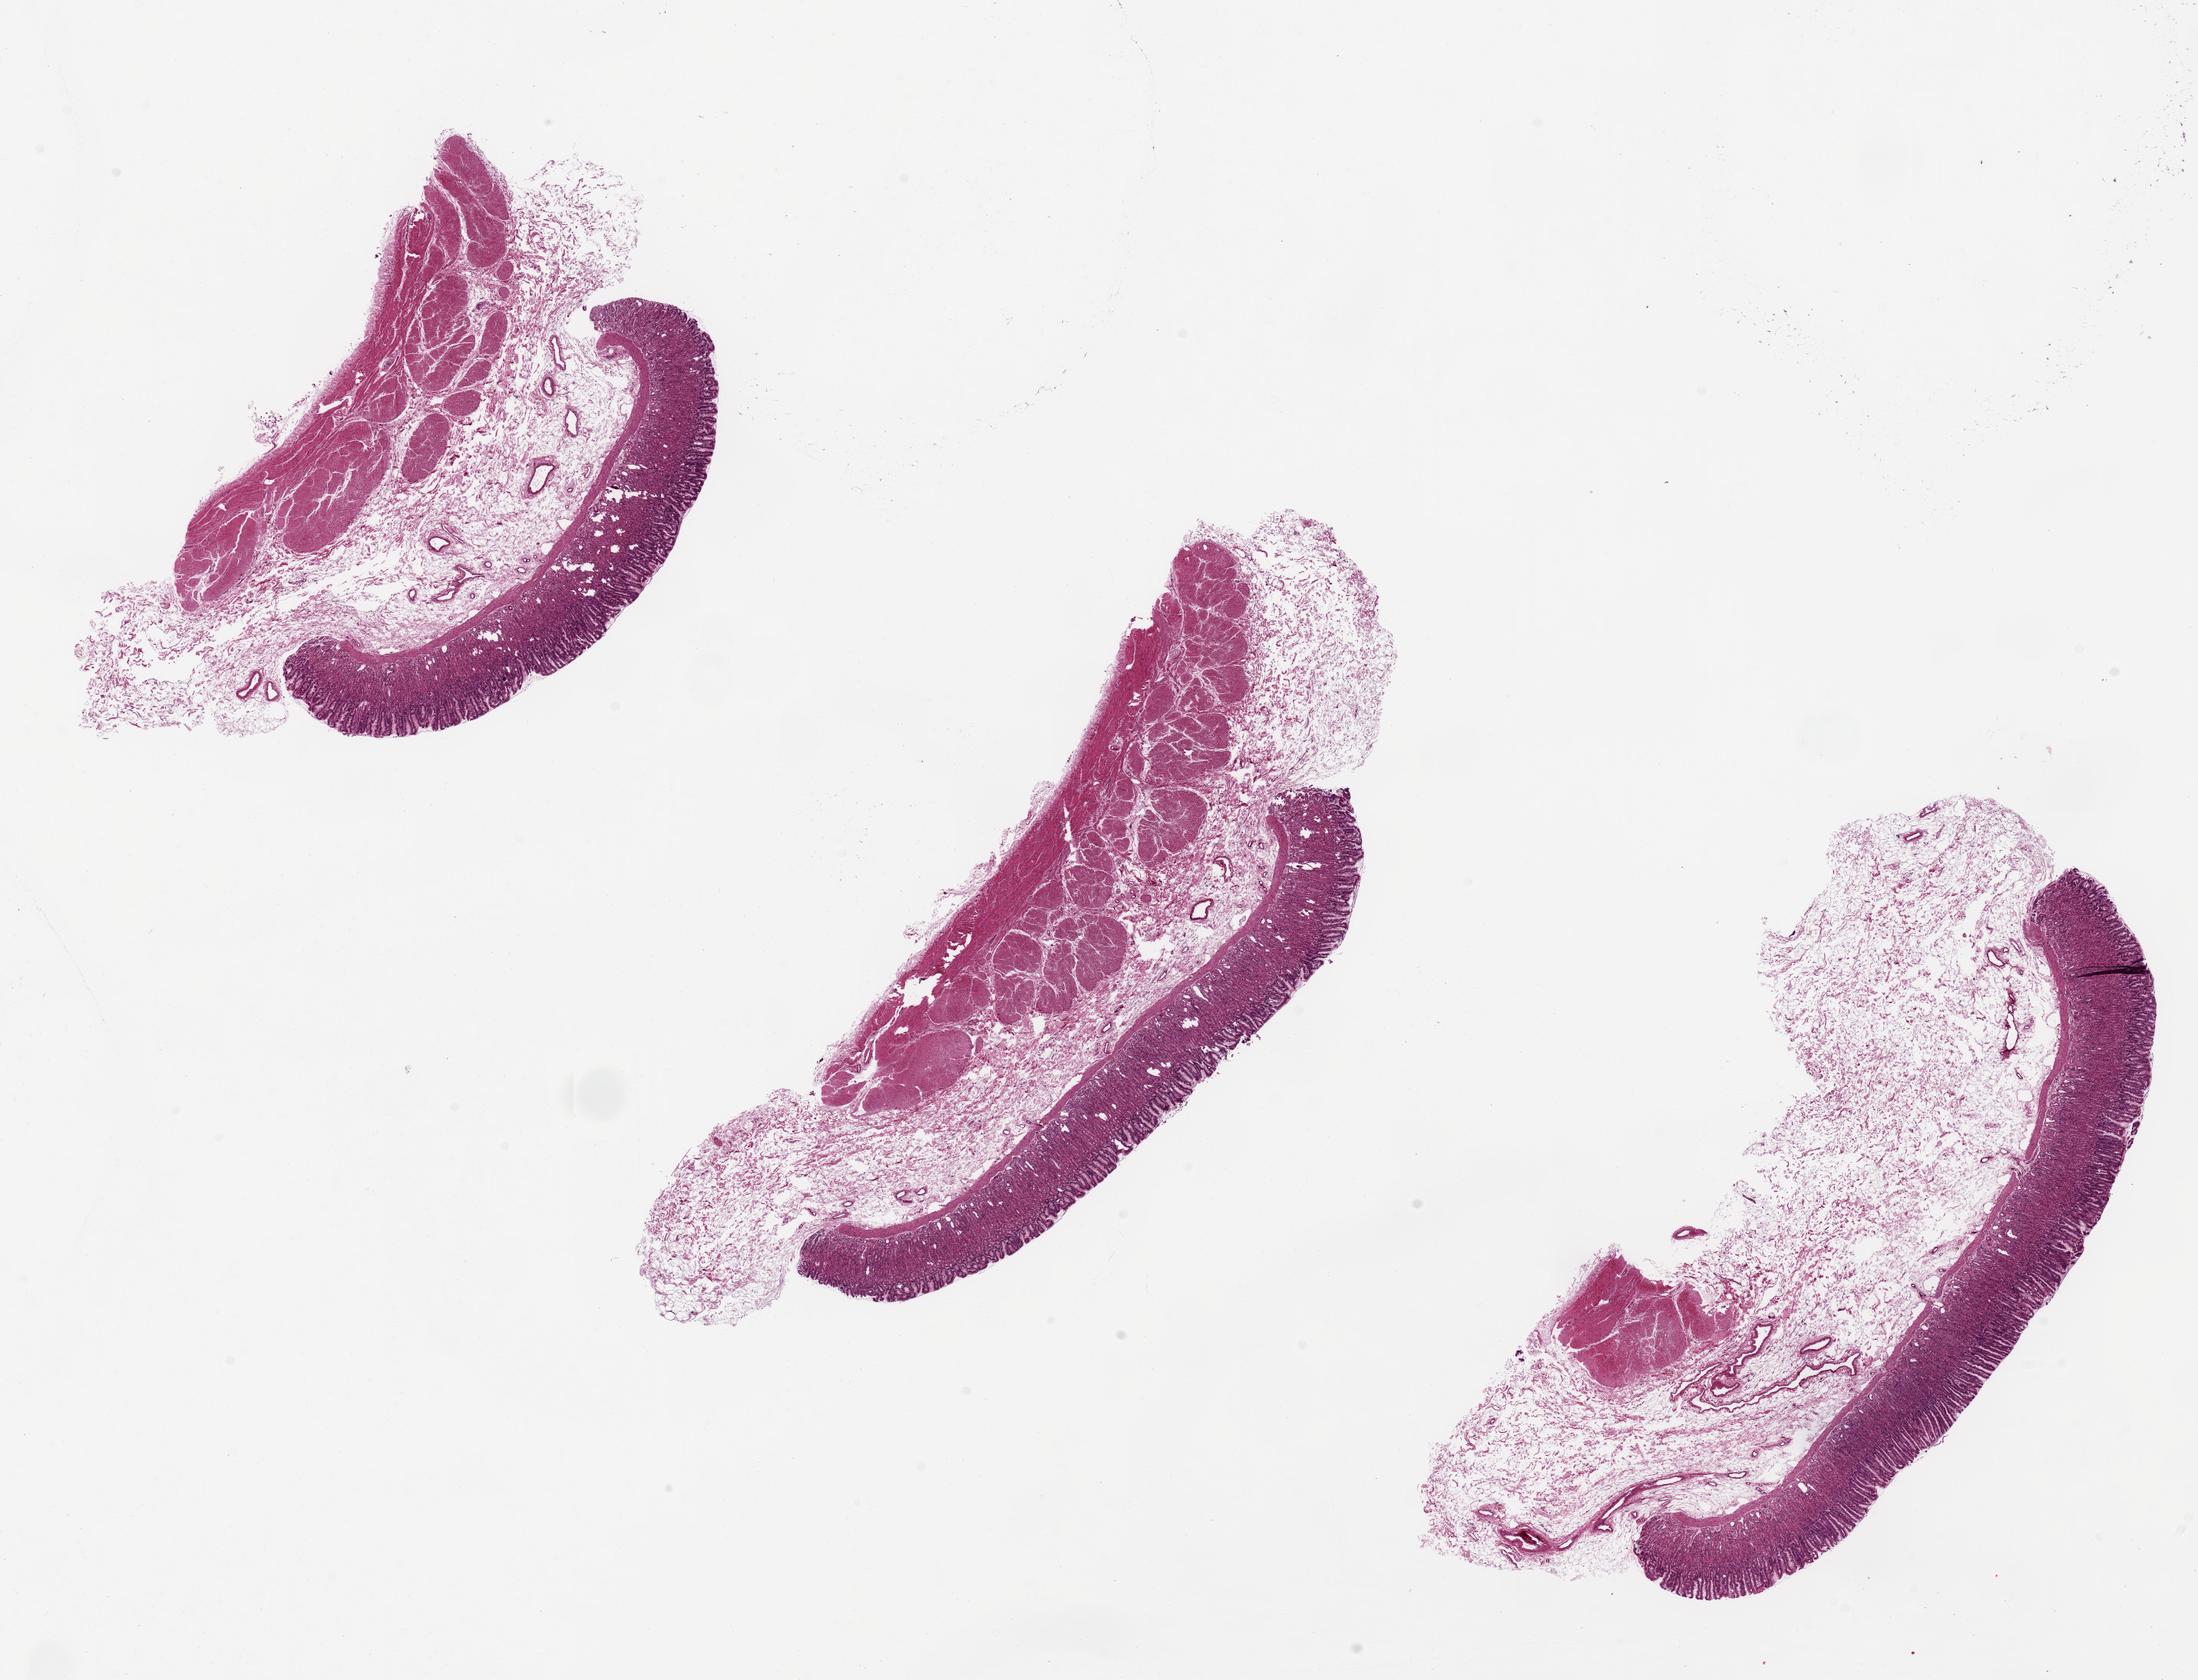
Digitized H&E-stained section, brightfield, a low-resolution overview of the entire scanned area, about 22.6 x 17.3 mm (from a 20x scan), PAXgene-fixed paraffin-embedded (PFPE) section, target tissue: stomach, tissue donor sample. Donor sex: female.
* reviewer comment on this tissue sample: 3 ~8x3mm pieces. Foveolar cells focally simulate intestinal metaplasia because of their mucous vacuoles, but they are too regular and apical, rarely barrel-shaped; without dysplasia. Mucosa is ~20-25% of specimen thickness. No sign of an inflammatory infiltrate or atrophy of the glandular cells